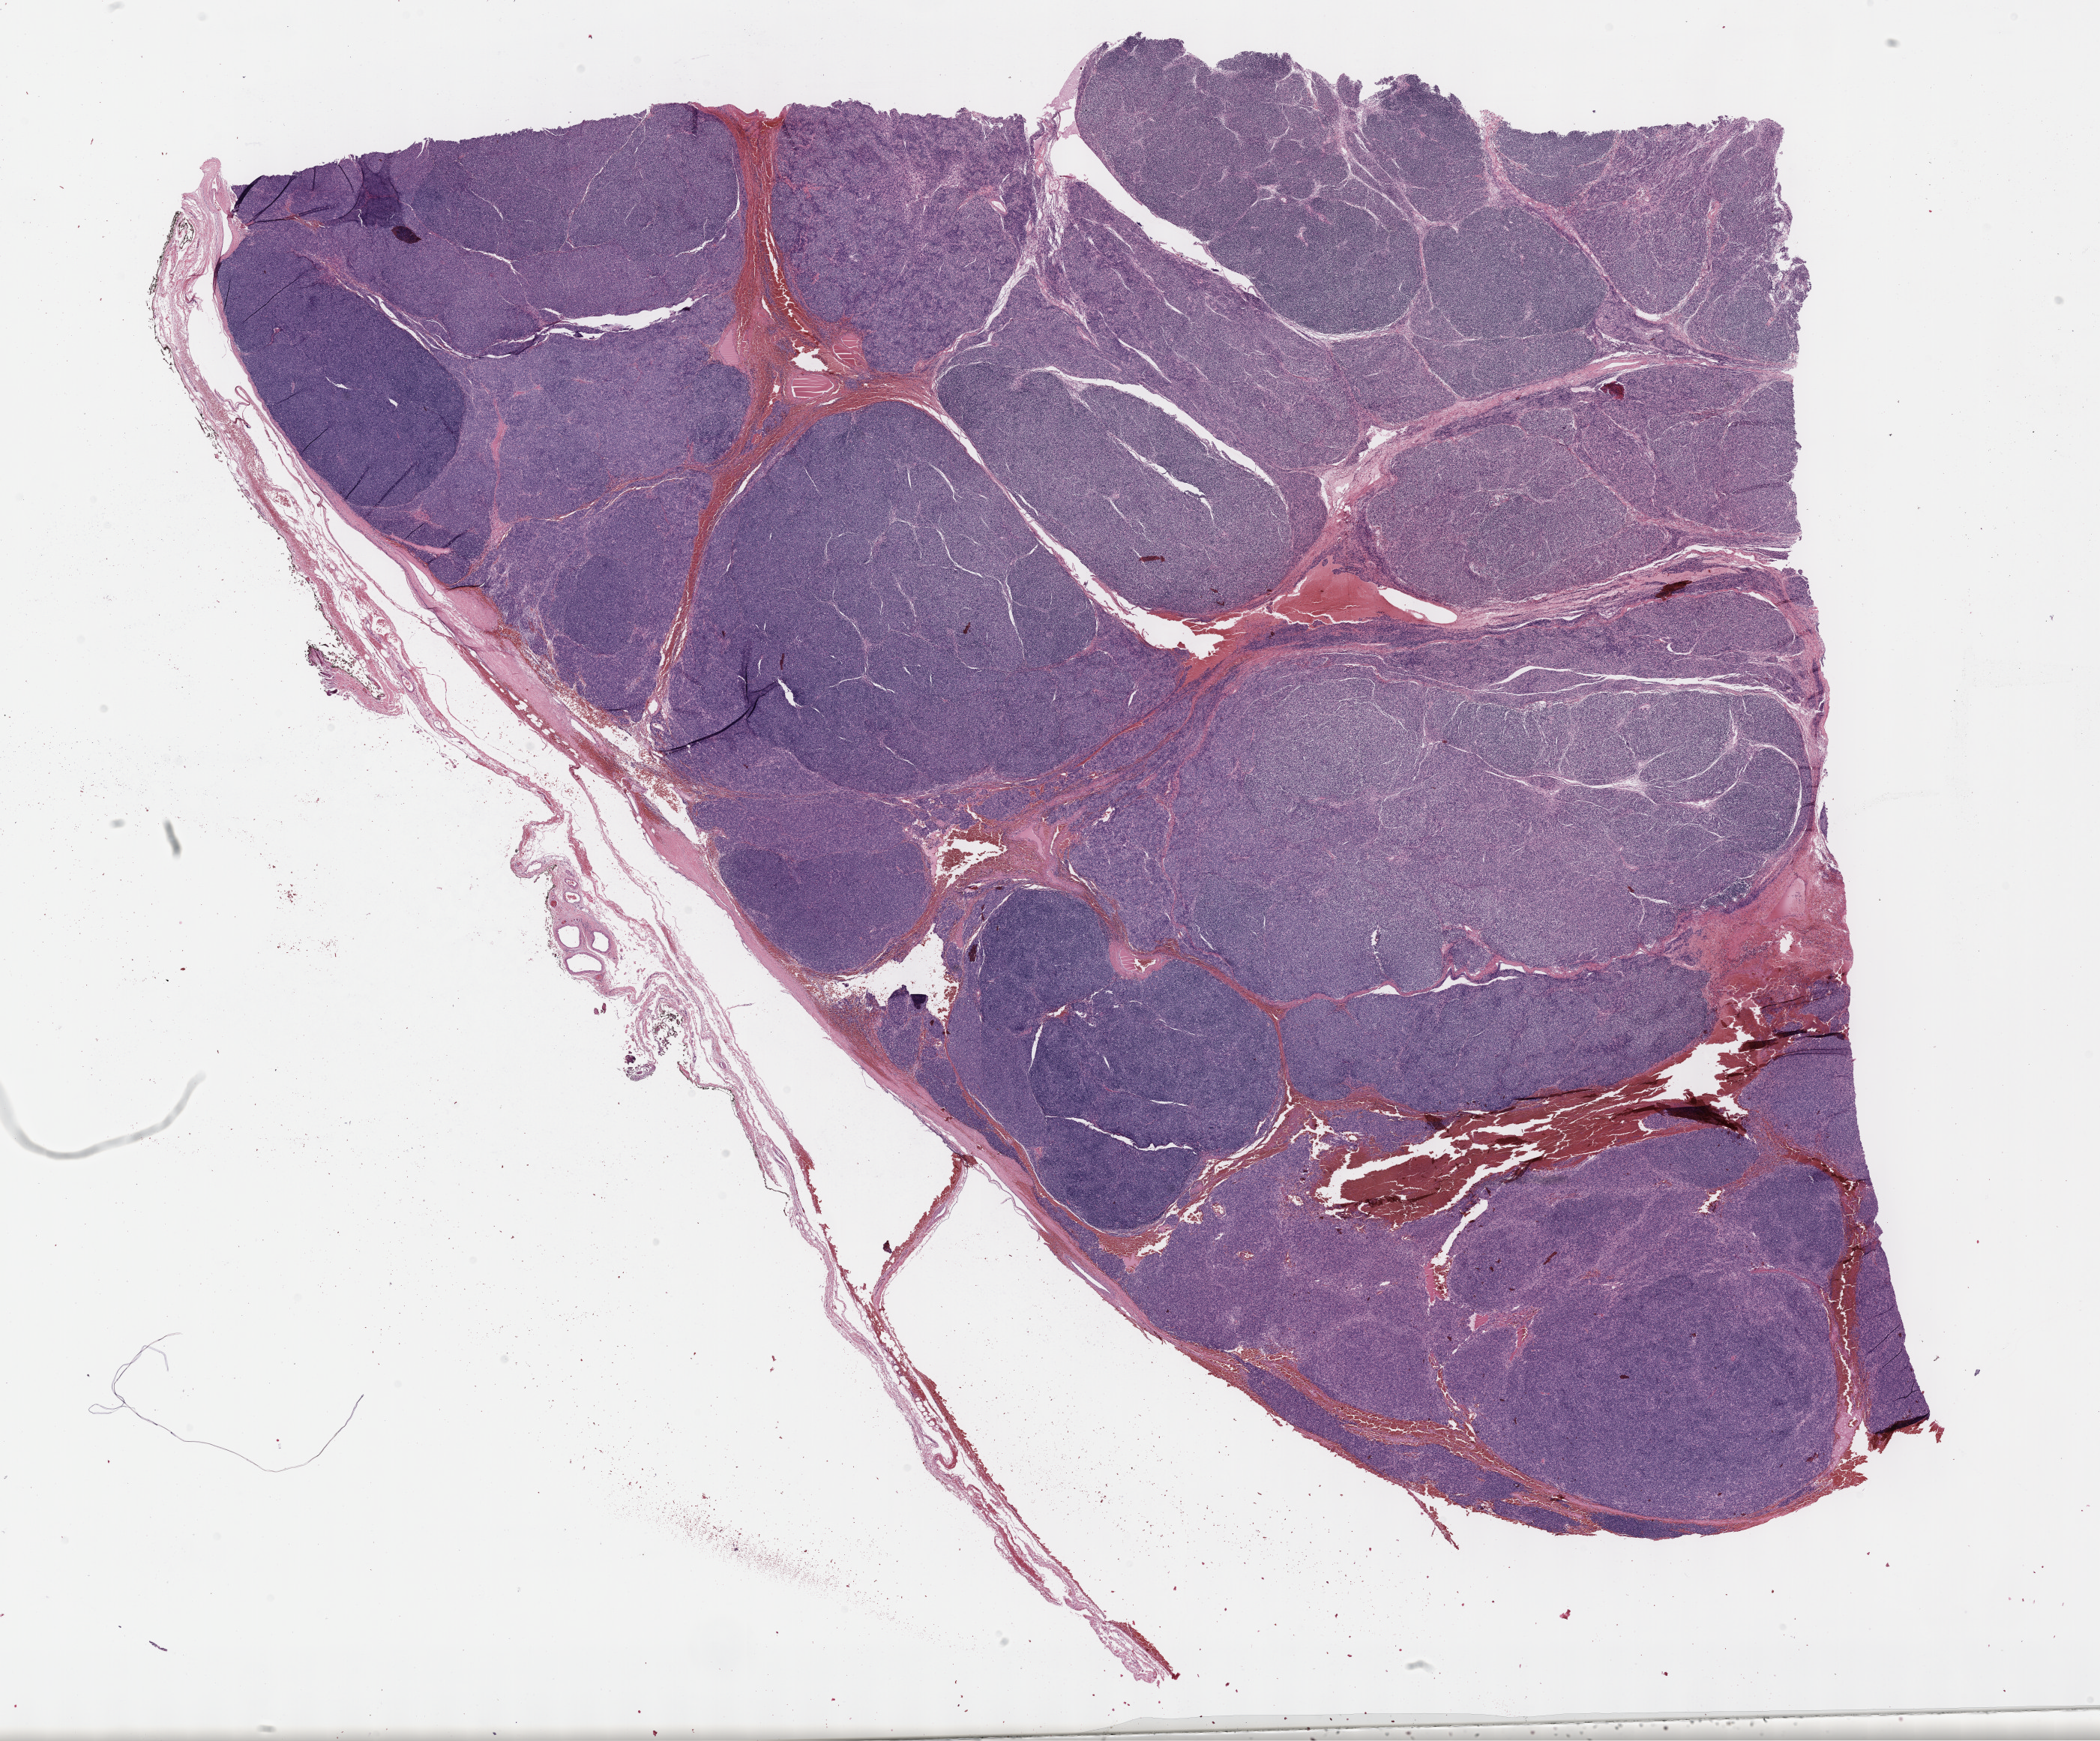
H&E-stained whole-slide image, a low-resolution overview of the entire scanned area, about 22.7 x 18.8 mm, formalin-fixed paraffin-embedded (FFPE) diagnostic section, primary tumour sample from the thymus. Female patient; age at initial diagnosis 55 years.
Pathologic diagnosis: Thymoma, type AB, NOS (anterior mediastinum).